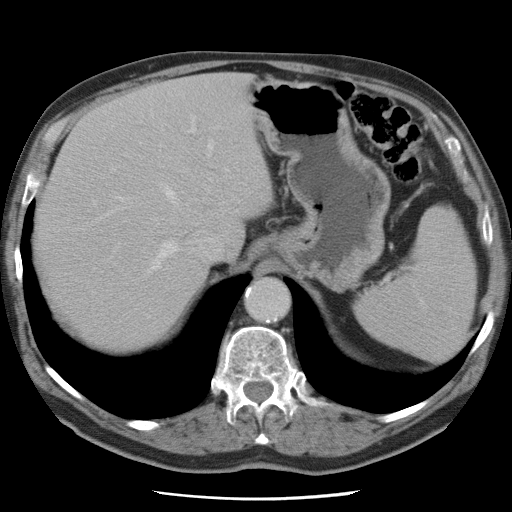
Contrast-enhanced abdominal CT, one axial slice. Position 58 of 78 along the scan axis. 120 kVp. Intravenous contrast given. Soft-tissue window (W 400 / L 40 HU). 5 mm slice thickness. 512 × 512 image matrix, field of view 337 × 337 mm. Male patient, age 75 years. From the clinical record (not read from this slice): diagnosis: colorectal cancer liver metastases, imaged before liver resection; multiple liver metastases: yes; largest metastasis: 2.4 cm; chemotherapy before resection: yes.
Annotated regions visible in this slice (expert manual segmentation):
- hepatic veins: box from (x=93, y=128) to (x=217, y=274) px
- liver: (x=37, y=74)–(x=271, y=348)
- planned liver remnant (the part of the liver to remain after resection): (x=37, y=131)–(x=206, y=347)
- portal vein (with intrahepatic branches): (x=111, y=169)–(x=128, y=253)